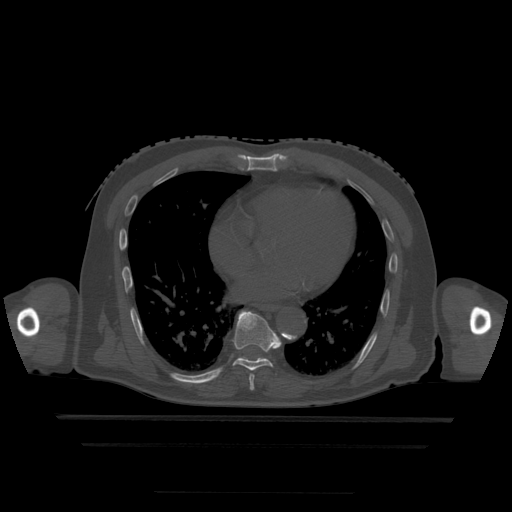
CT including the spine, one axial slice. Bone window (W 1800 / L 400 HU). 1.25 mm slice thickness. 512 × 512 image matrix. Patient age 68 years. Case-level facts recorded for this patient, not image findings: primary cancer: urothelial.
Outlined on this slice (semi-automatic segmentation, software-assisted and operator-edited):
- T7 vertebra: bounding box (x1, y1, x2, y2) in pixels: (249, 375, 255, 391)
- T8 vertebra: (233, 310, 282, 371)
- T9 vertebra: (239, 357, 265, 361)